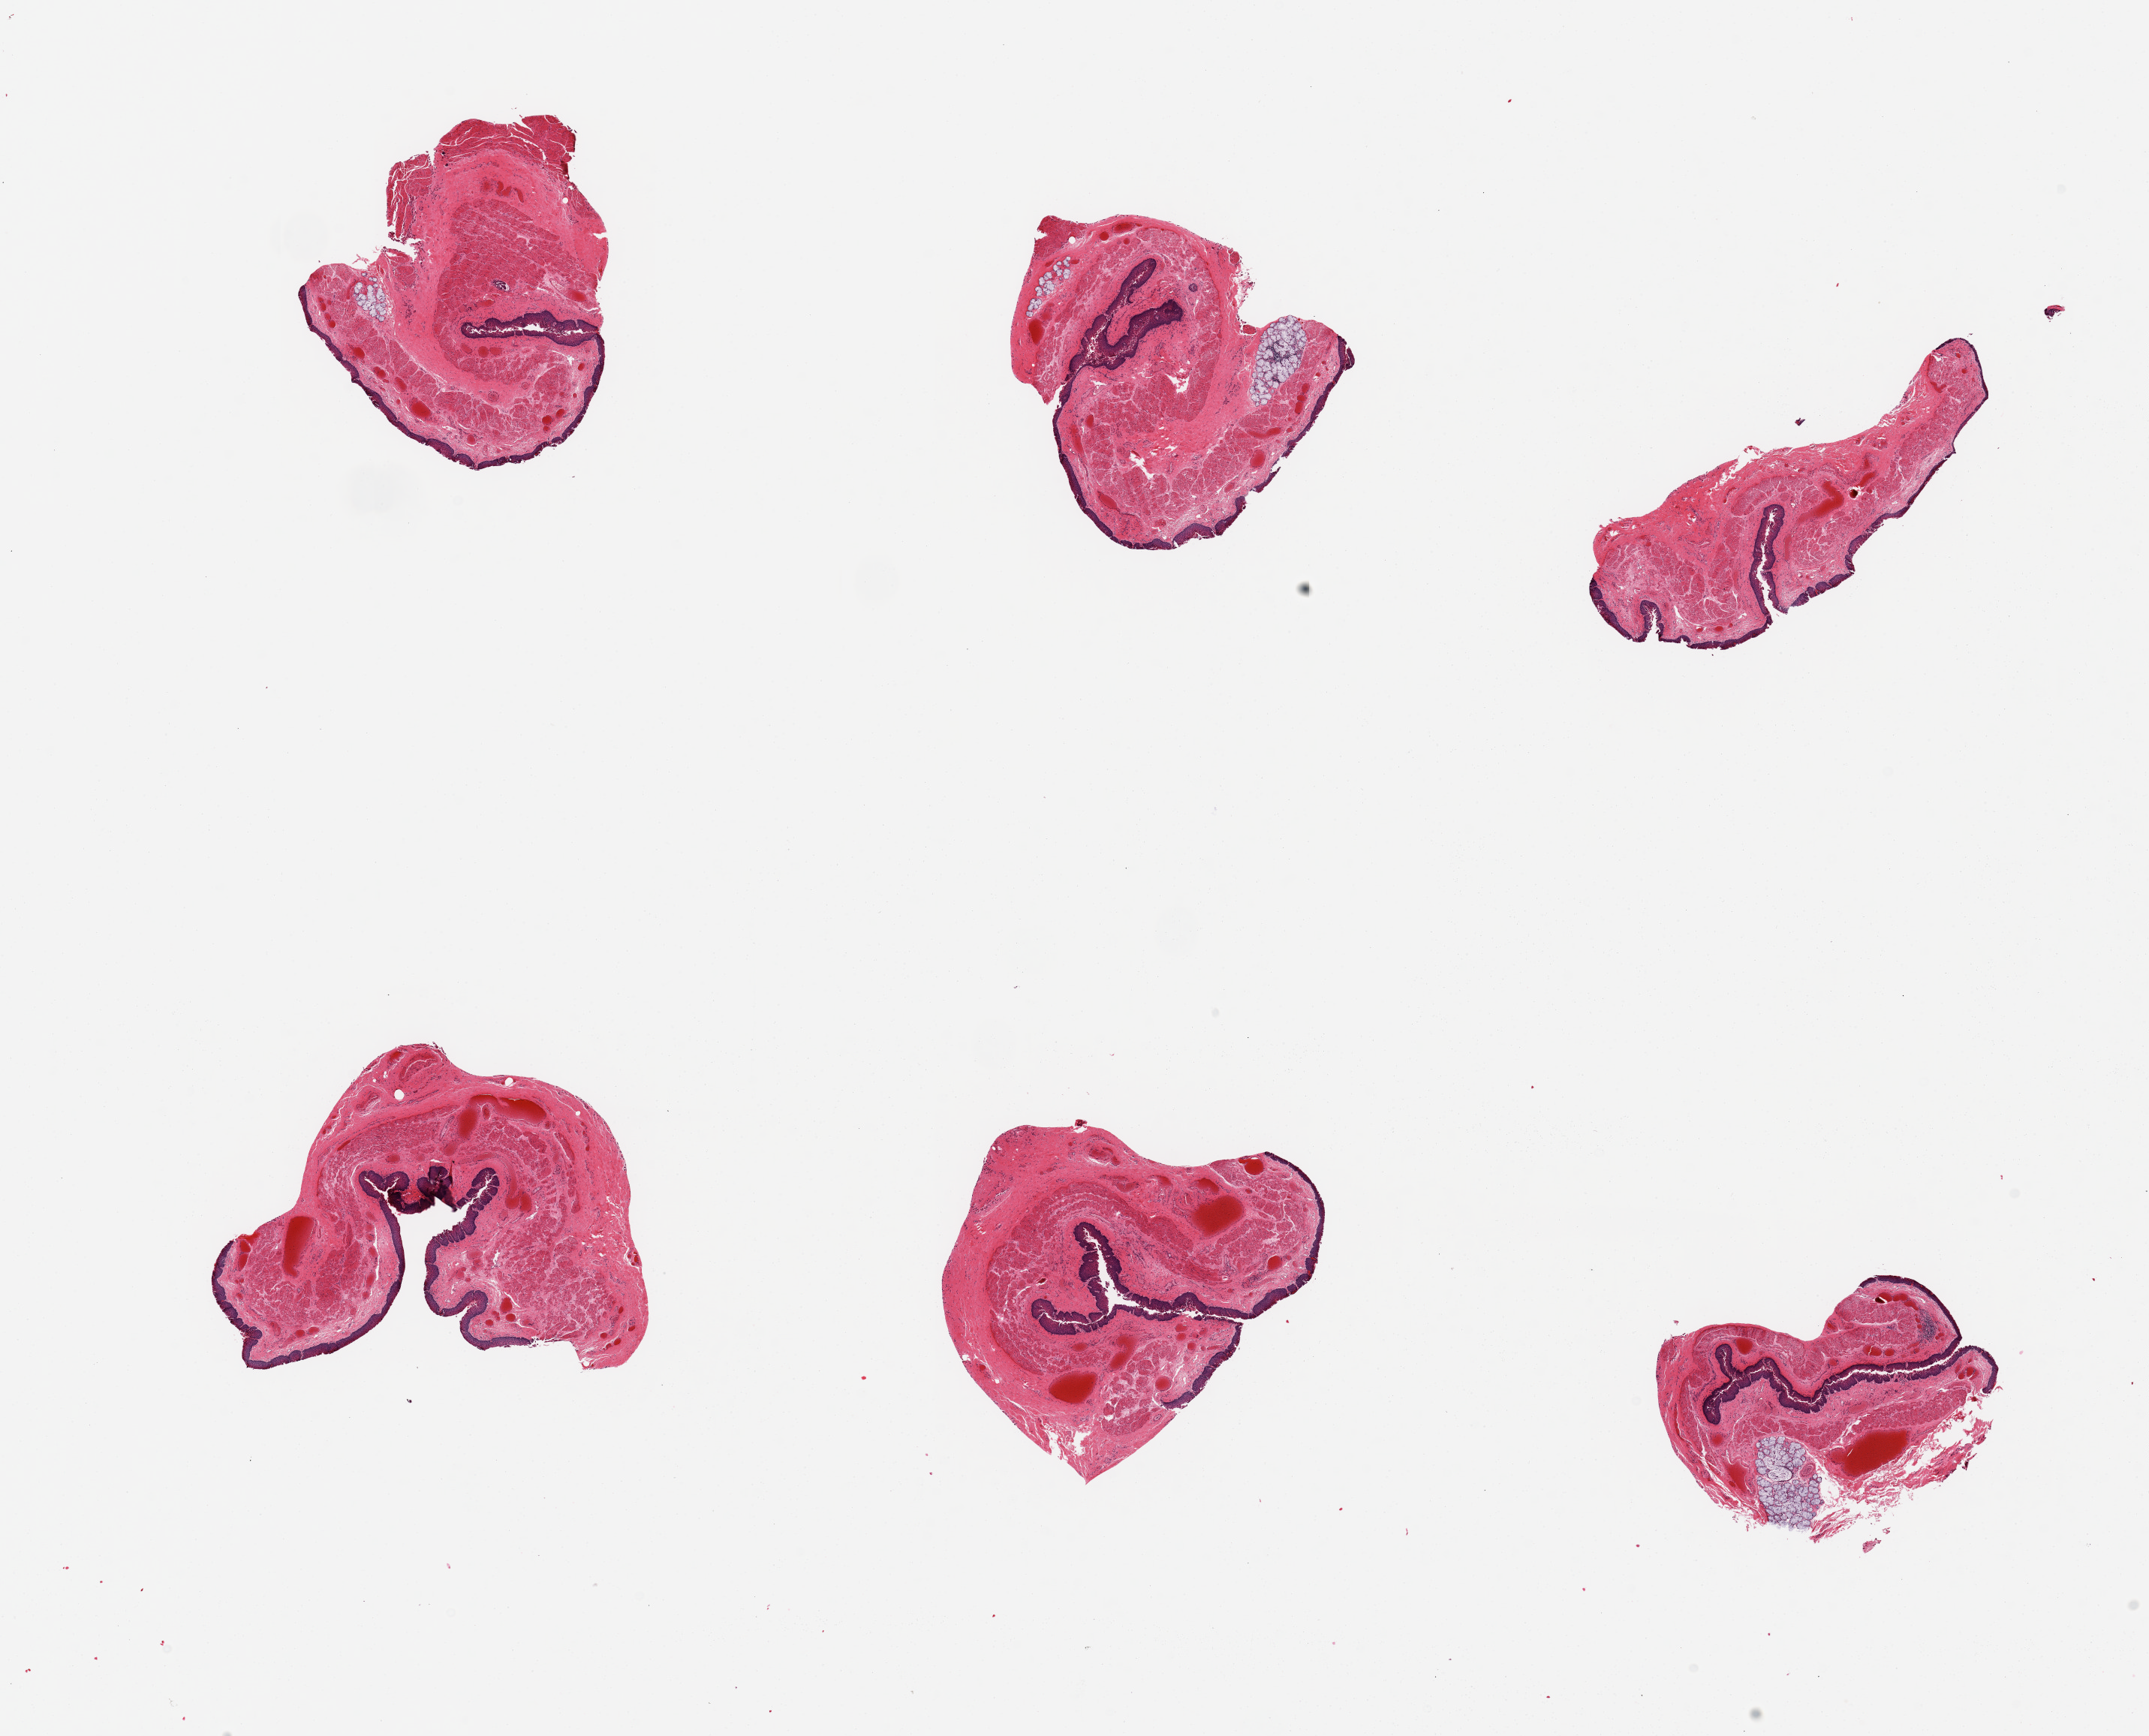
Whole-slide image, H&E stain — shown as a low-resolution overview of the whole scanned area (about 22.6 x 18.3 mm), PAXgene-fixed, paraffin-embedded tissue, target tissue: esophageal mucous membrane, donor tissue sample. Donor: male.
Pathologist's review note for this sample: 6 pieces; submucosal gland in 3 pieces up to 1 mm.